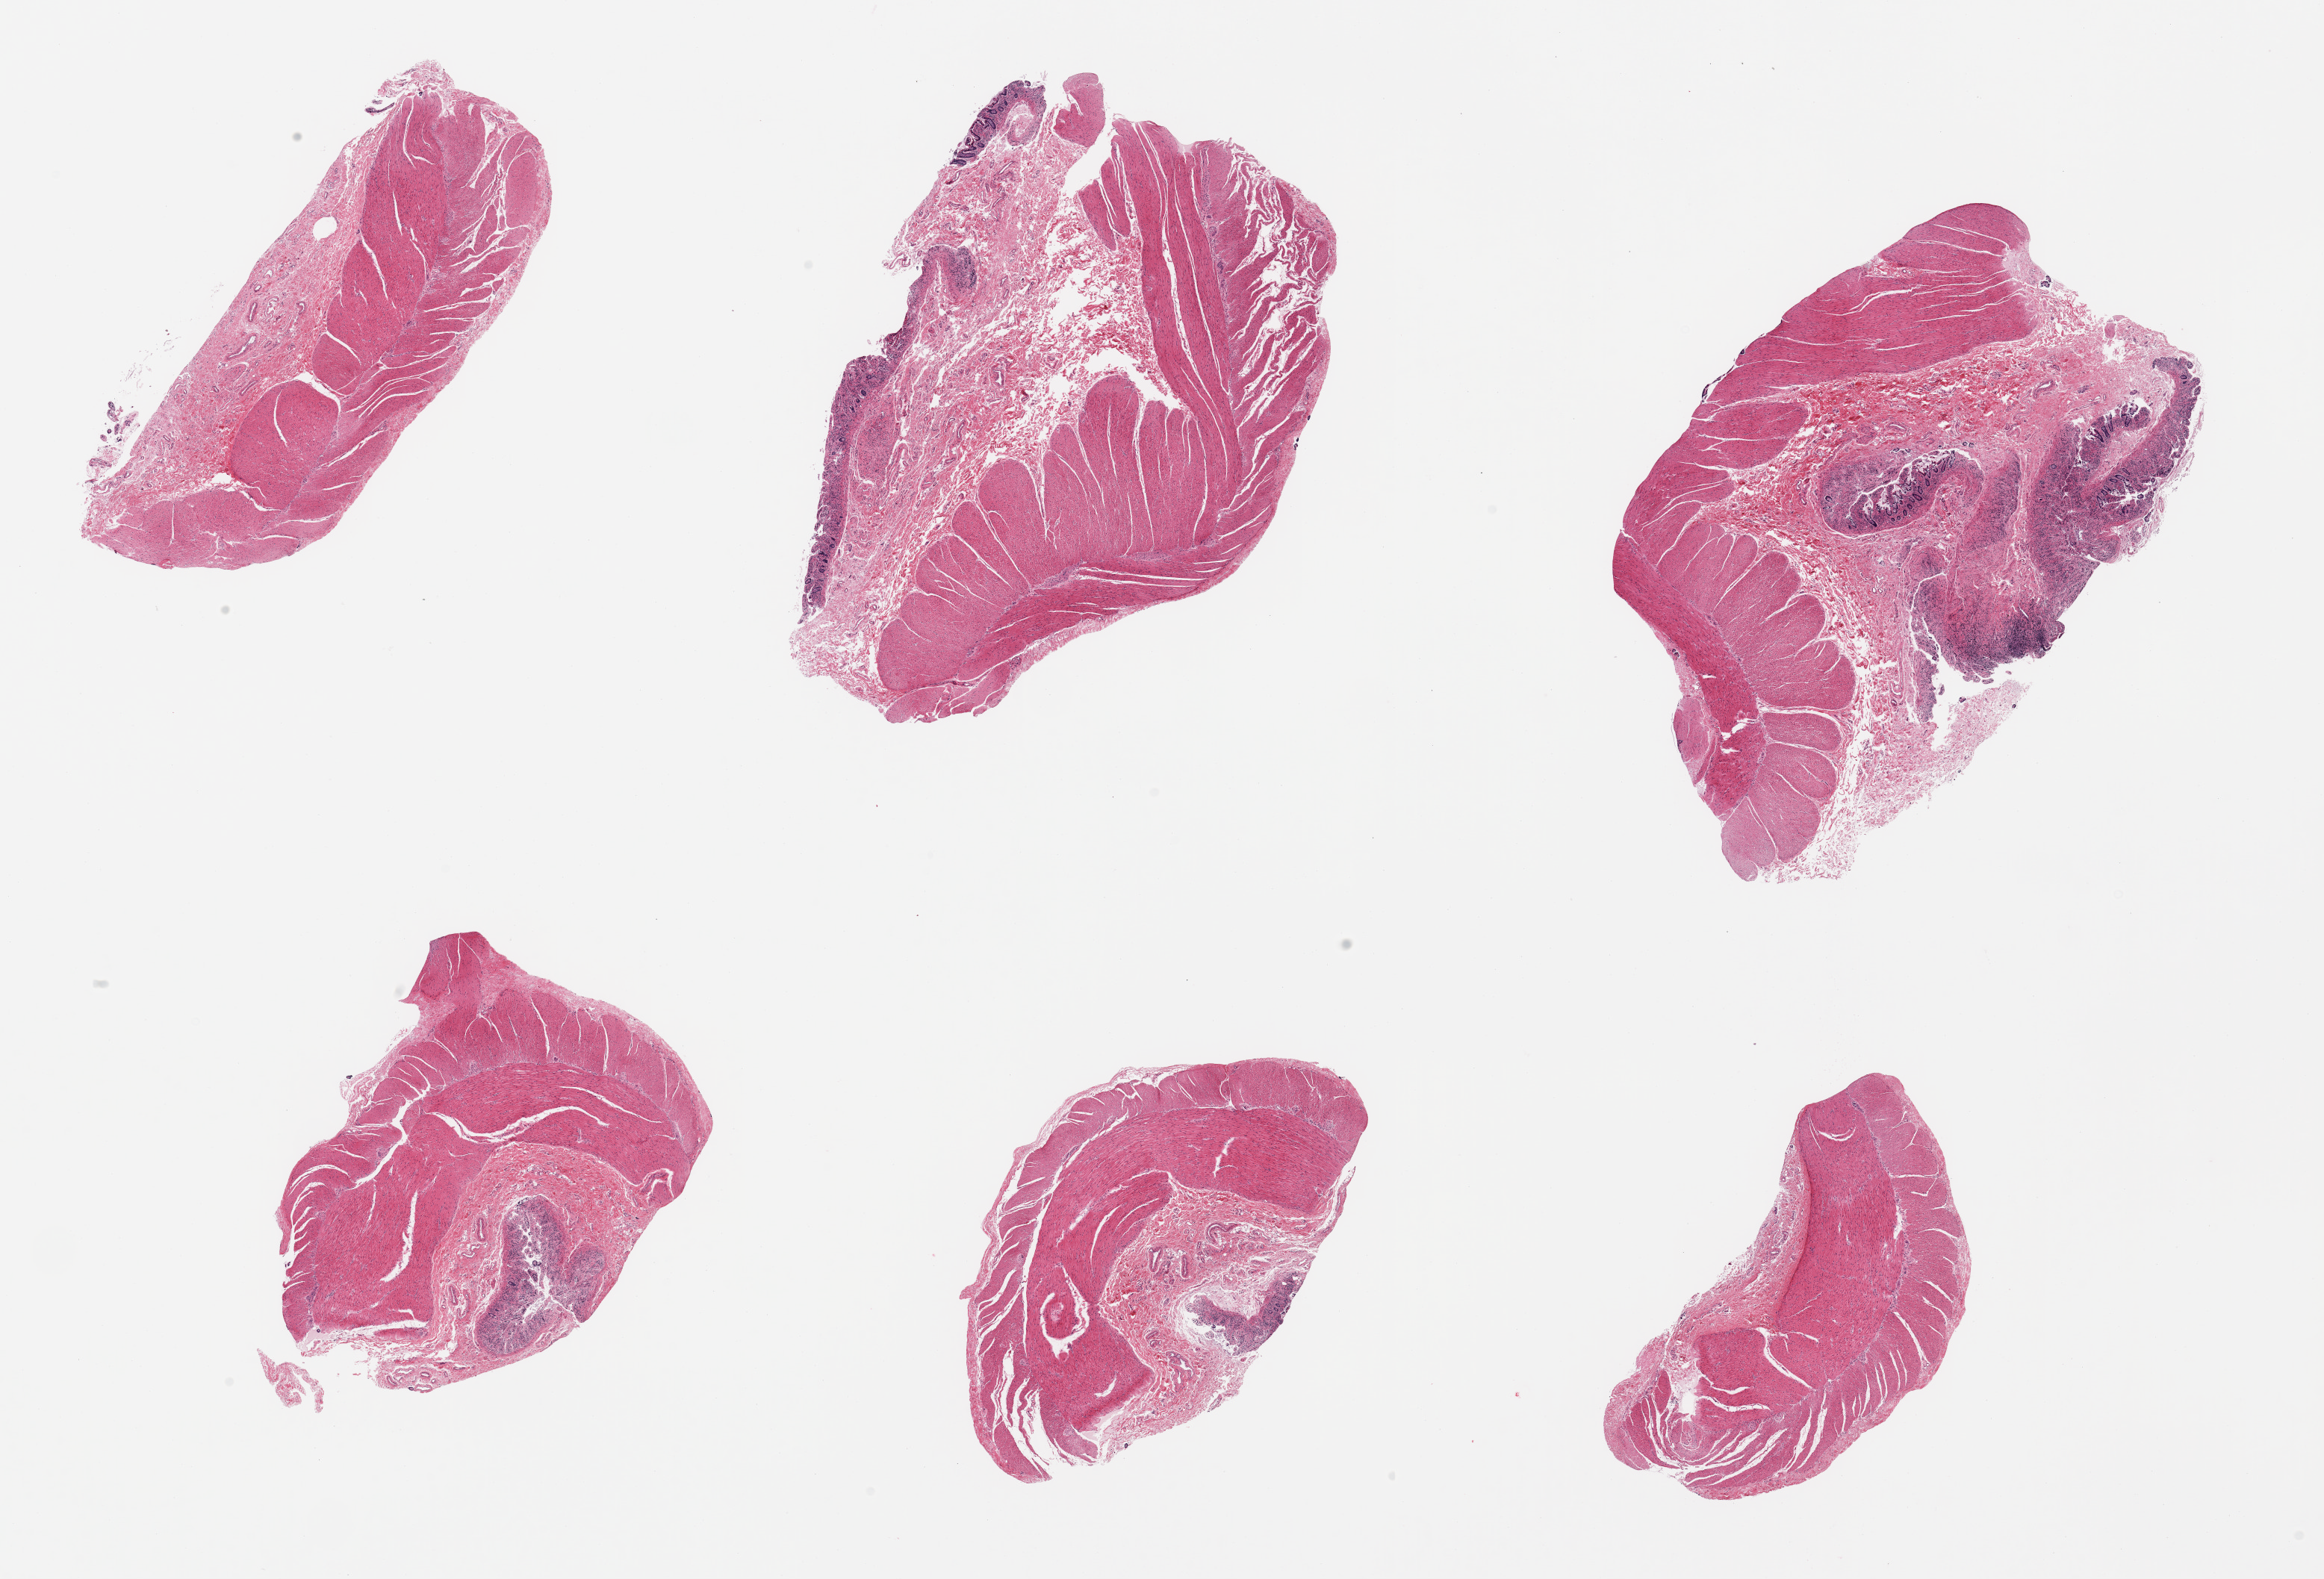
Digitized H&E-stained section, brightfield — a low-resolution overview of the entire scanned area, about 24.6 x 16.7 mm (slide scanned at 20x). PAXgene-fixed paraffin-embedded (PFPE) section. Sampled site (target tissue): ileum. Donor tissue sample. Male donor.
* review note (as recorded): 6 pieces, mainly muscularis, trace autolyzed mucosa, insufficient lymphoid aggregate for analysis